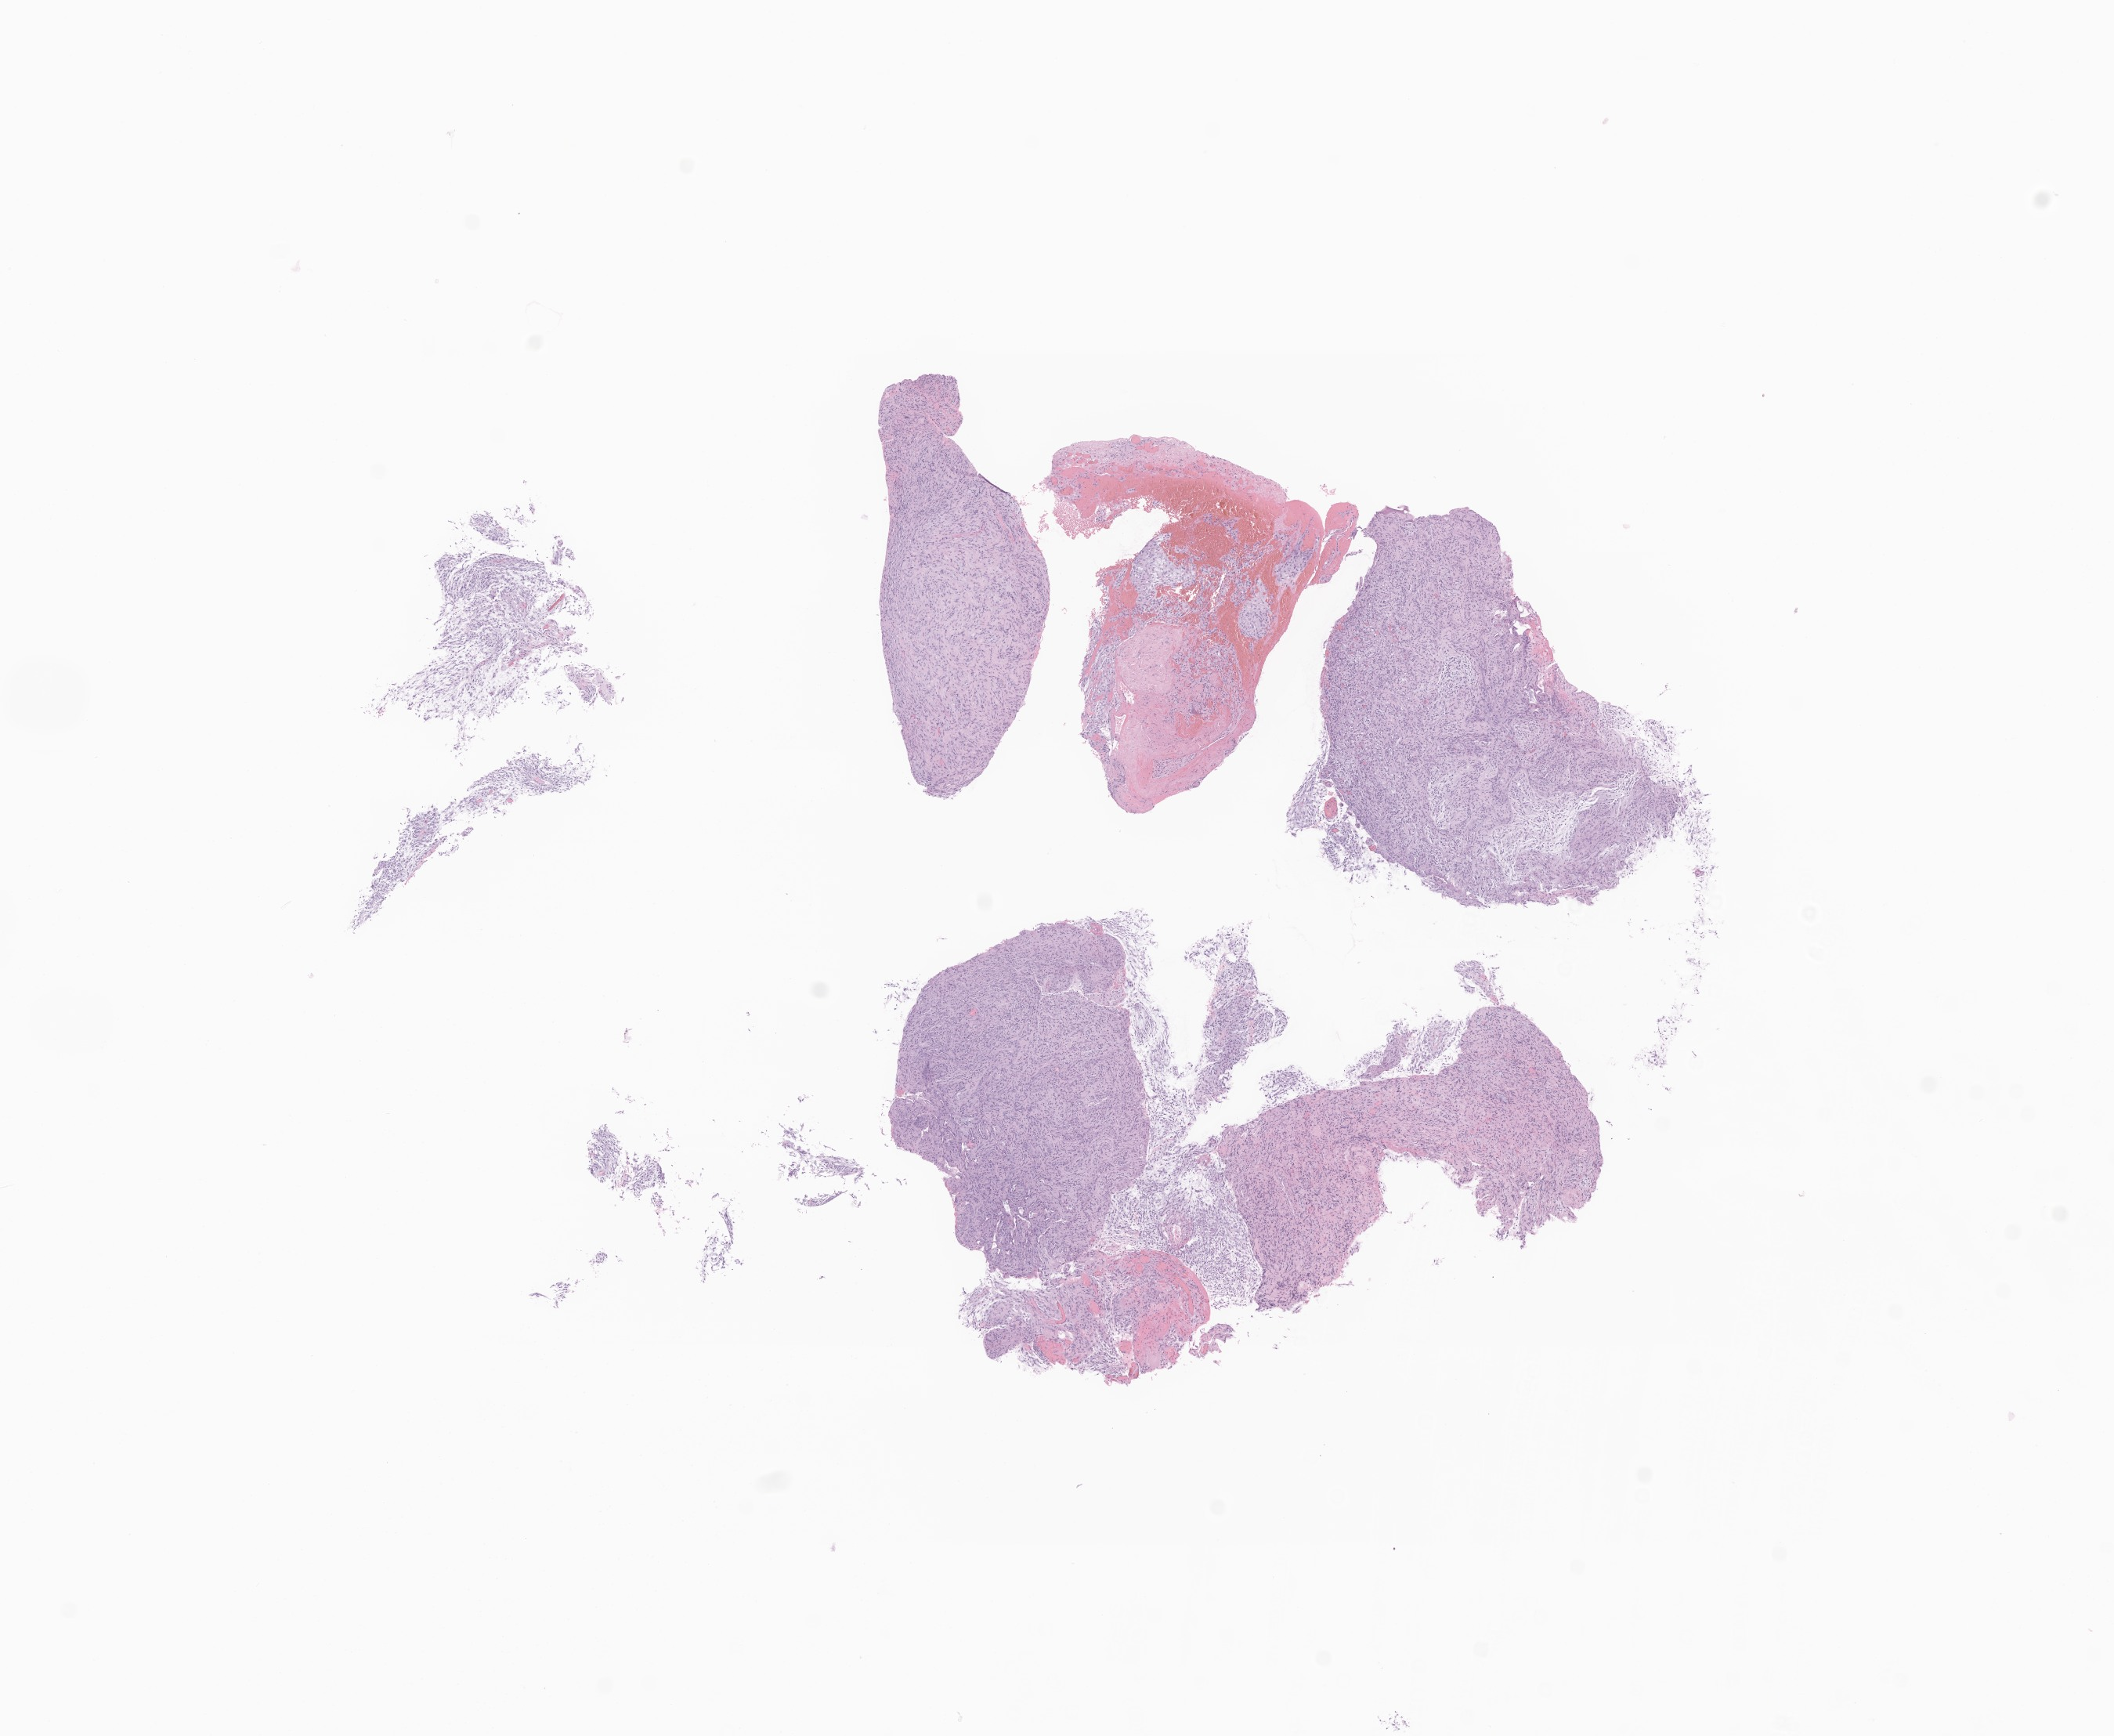
Digitized H&E-stained section of tumor tissue from the brain — a low-resolution overview of the entire scanned area, about 11.4 x 9.3 mm, FFPE section. Patient male; age 298 days.
Diagnosis (ICD-O-3 morphology term): Pilocytic astrocytoma.